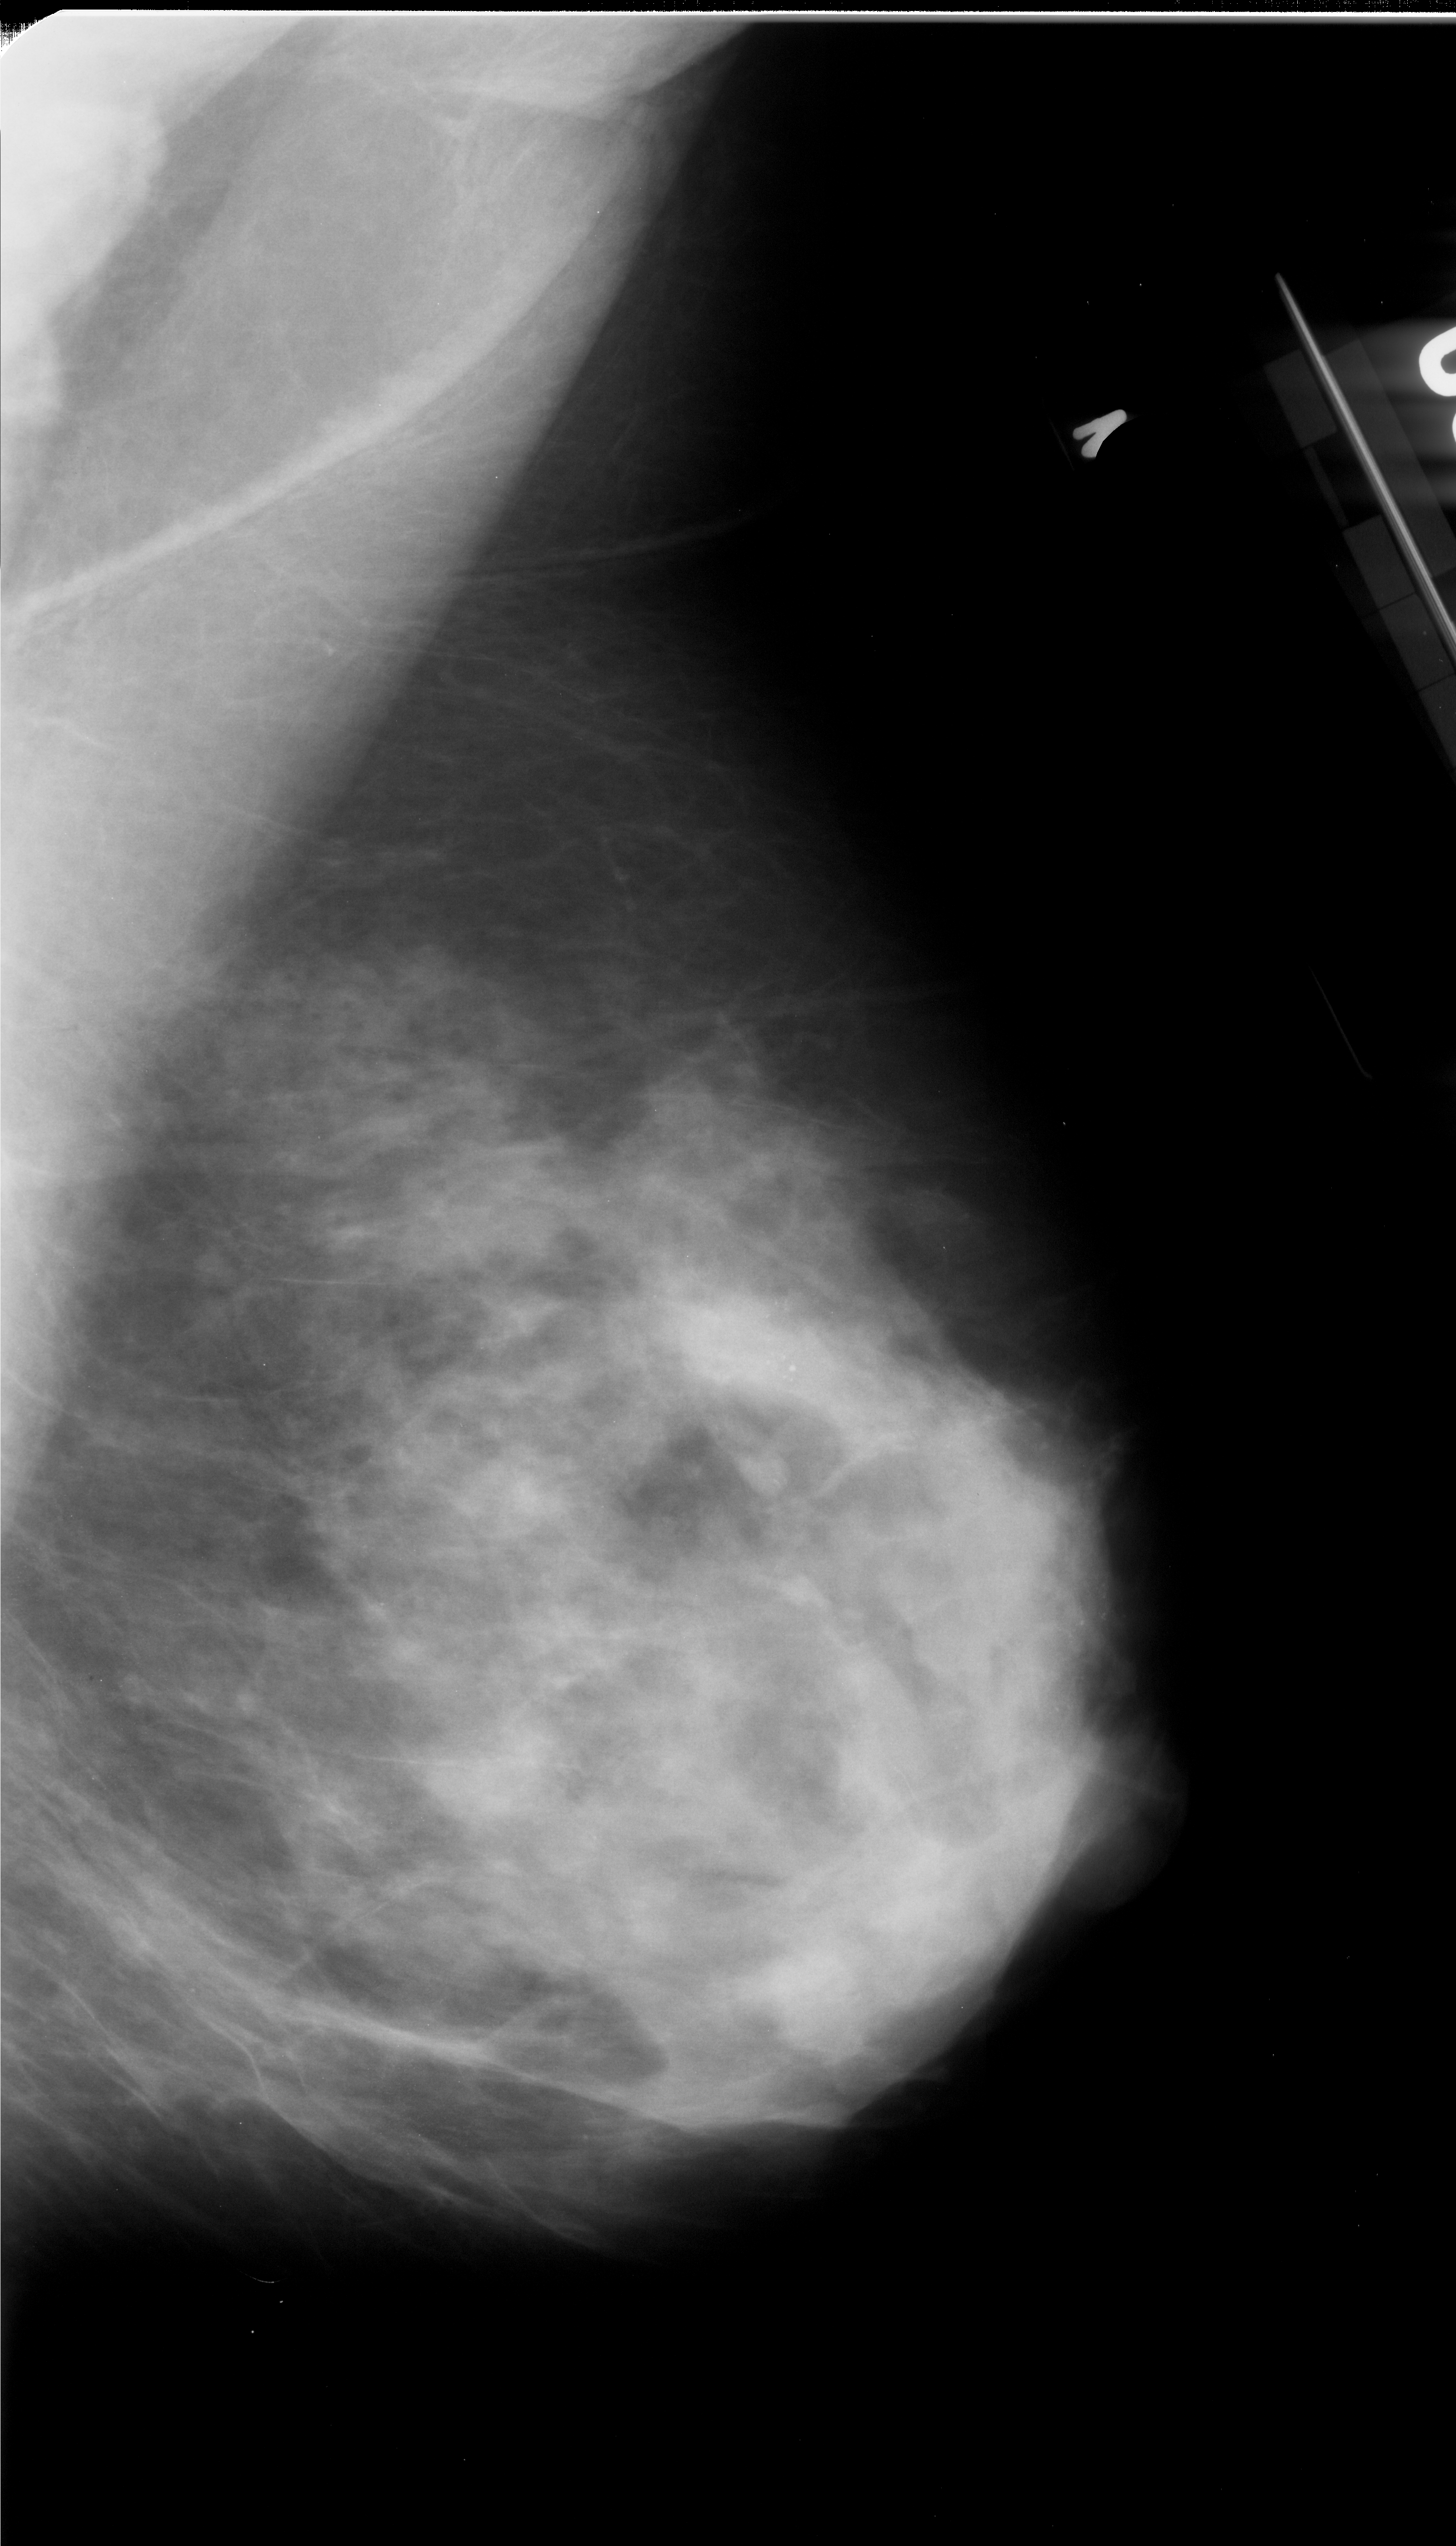
Mammogram (digitized film). Right breast. Mediolateral oblique (MLO) view. Breast composition: extremely dense (BI-RADS density category 4 of 4). 1456 × 2546 image matrix.
Expert-marked regions of interest on this image (one box per marked abnormality):
- calcifications, morphology pleomorphic, distribution clustered; BI-RADS assessment category 4; subtlety rating 3 on a 1 (subtle) to 5 (obvious) scale; pathology (as recorded): malignant: bounding box <746,1279,810,1410> (left, top, right, bottom; pixels)